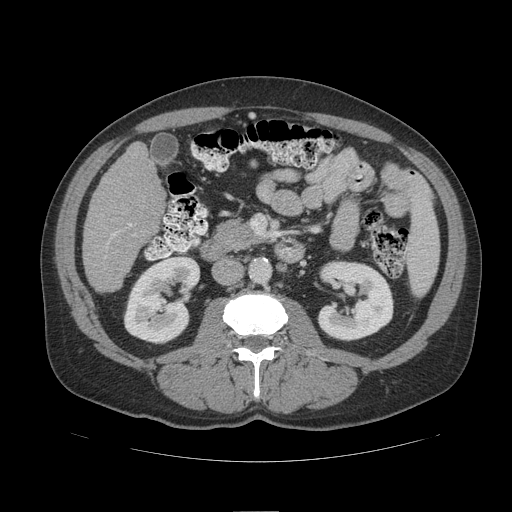
Contrast-enhanced abdominal CT (liver protocol), one axial slice; slice 39 of 109 in the series (ordered by position); 140 kVp; soft-tissue window (W 400 / L 40 HU); 2.5 mm slice thickness; 512 × 512 image matrix, field of view 420 × 420 mm. From the clinical record (not read from this slice): diagnosis: hepatocellular carcinoma (patient treated with transarterial chemoembolisation; whether this scan precedes or follows treatment is not stated here); TNM stage (as recorded): Stage-IIIB; Child-Pugh class: A; tumour nodularity: multinodular.
Annotated regions visible in this slice (semi-automatic segmentation, software-assisted and operator-edited):
- liver parenchyma outside the tumour (the mass and vessels are separate outlines, so this box may not span the whole liver): bounding box [x1, y1, x2, y2] px = [82, 142, 164, 292]
- liver vessels: [114, 224, 131, 235]